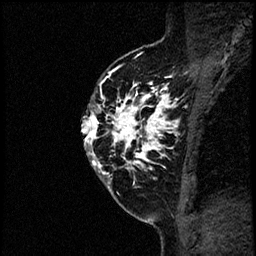
Breast MRI (dynamic contrast-enhanced), one sagittal slice; slice 42 of 60 in the series (ordered by position); dynamic contrast-enhanced study with each time point stored as its own series, time point 2 of 4 at this slice position (early post-contrast, ordered by acquisition time); 1.5 T; TE 4.2 ms, TR 17.6 ms; 256 × 256 image matrix, field of view 200 × 200 mm. Patient: female, 40 years. From the clinical record (not read from this slice): setting: breast cancer imaged before/during neoadjuvant chemotherapy; receptor status: HER2-positive.
Structures marked on this image (semi-automatically segmented with operator editing):
- analysis volume of interest (the breast-tissue region the enhancement analysis was run in; not a lesion): bounding box (x1, y1, x2, y2) in pixels: (83, 56, 197, 205)
- tumour enhancement mask (voxels above the 100 % enhancement threshold inside the analysis volume of interest): (83, 71, 179, 183)